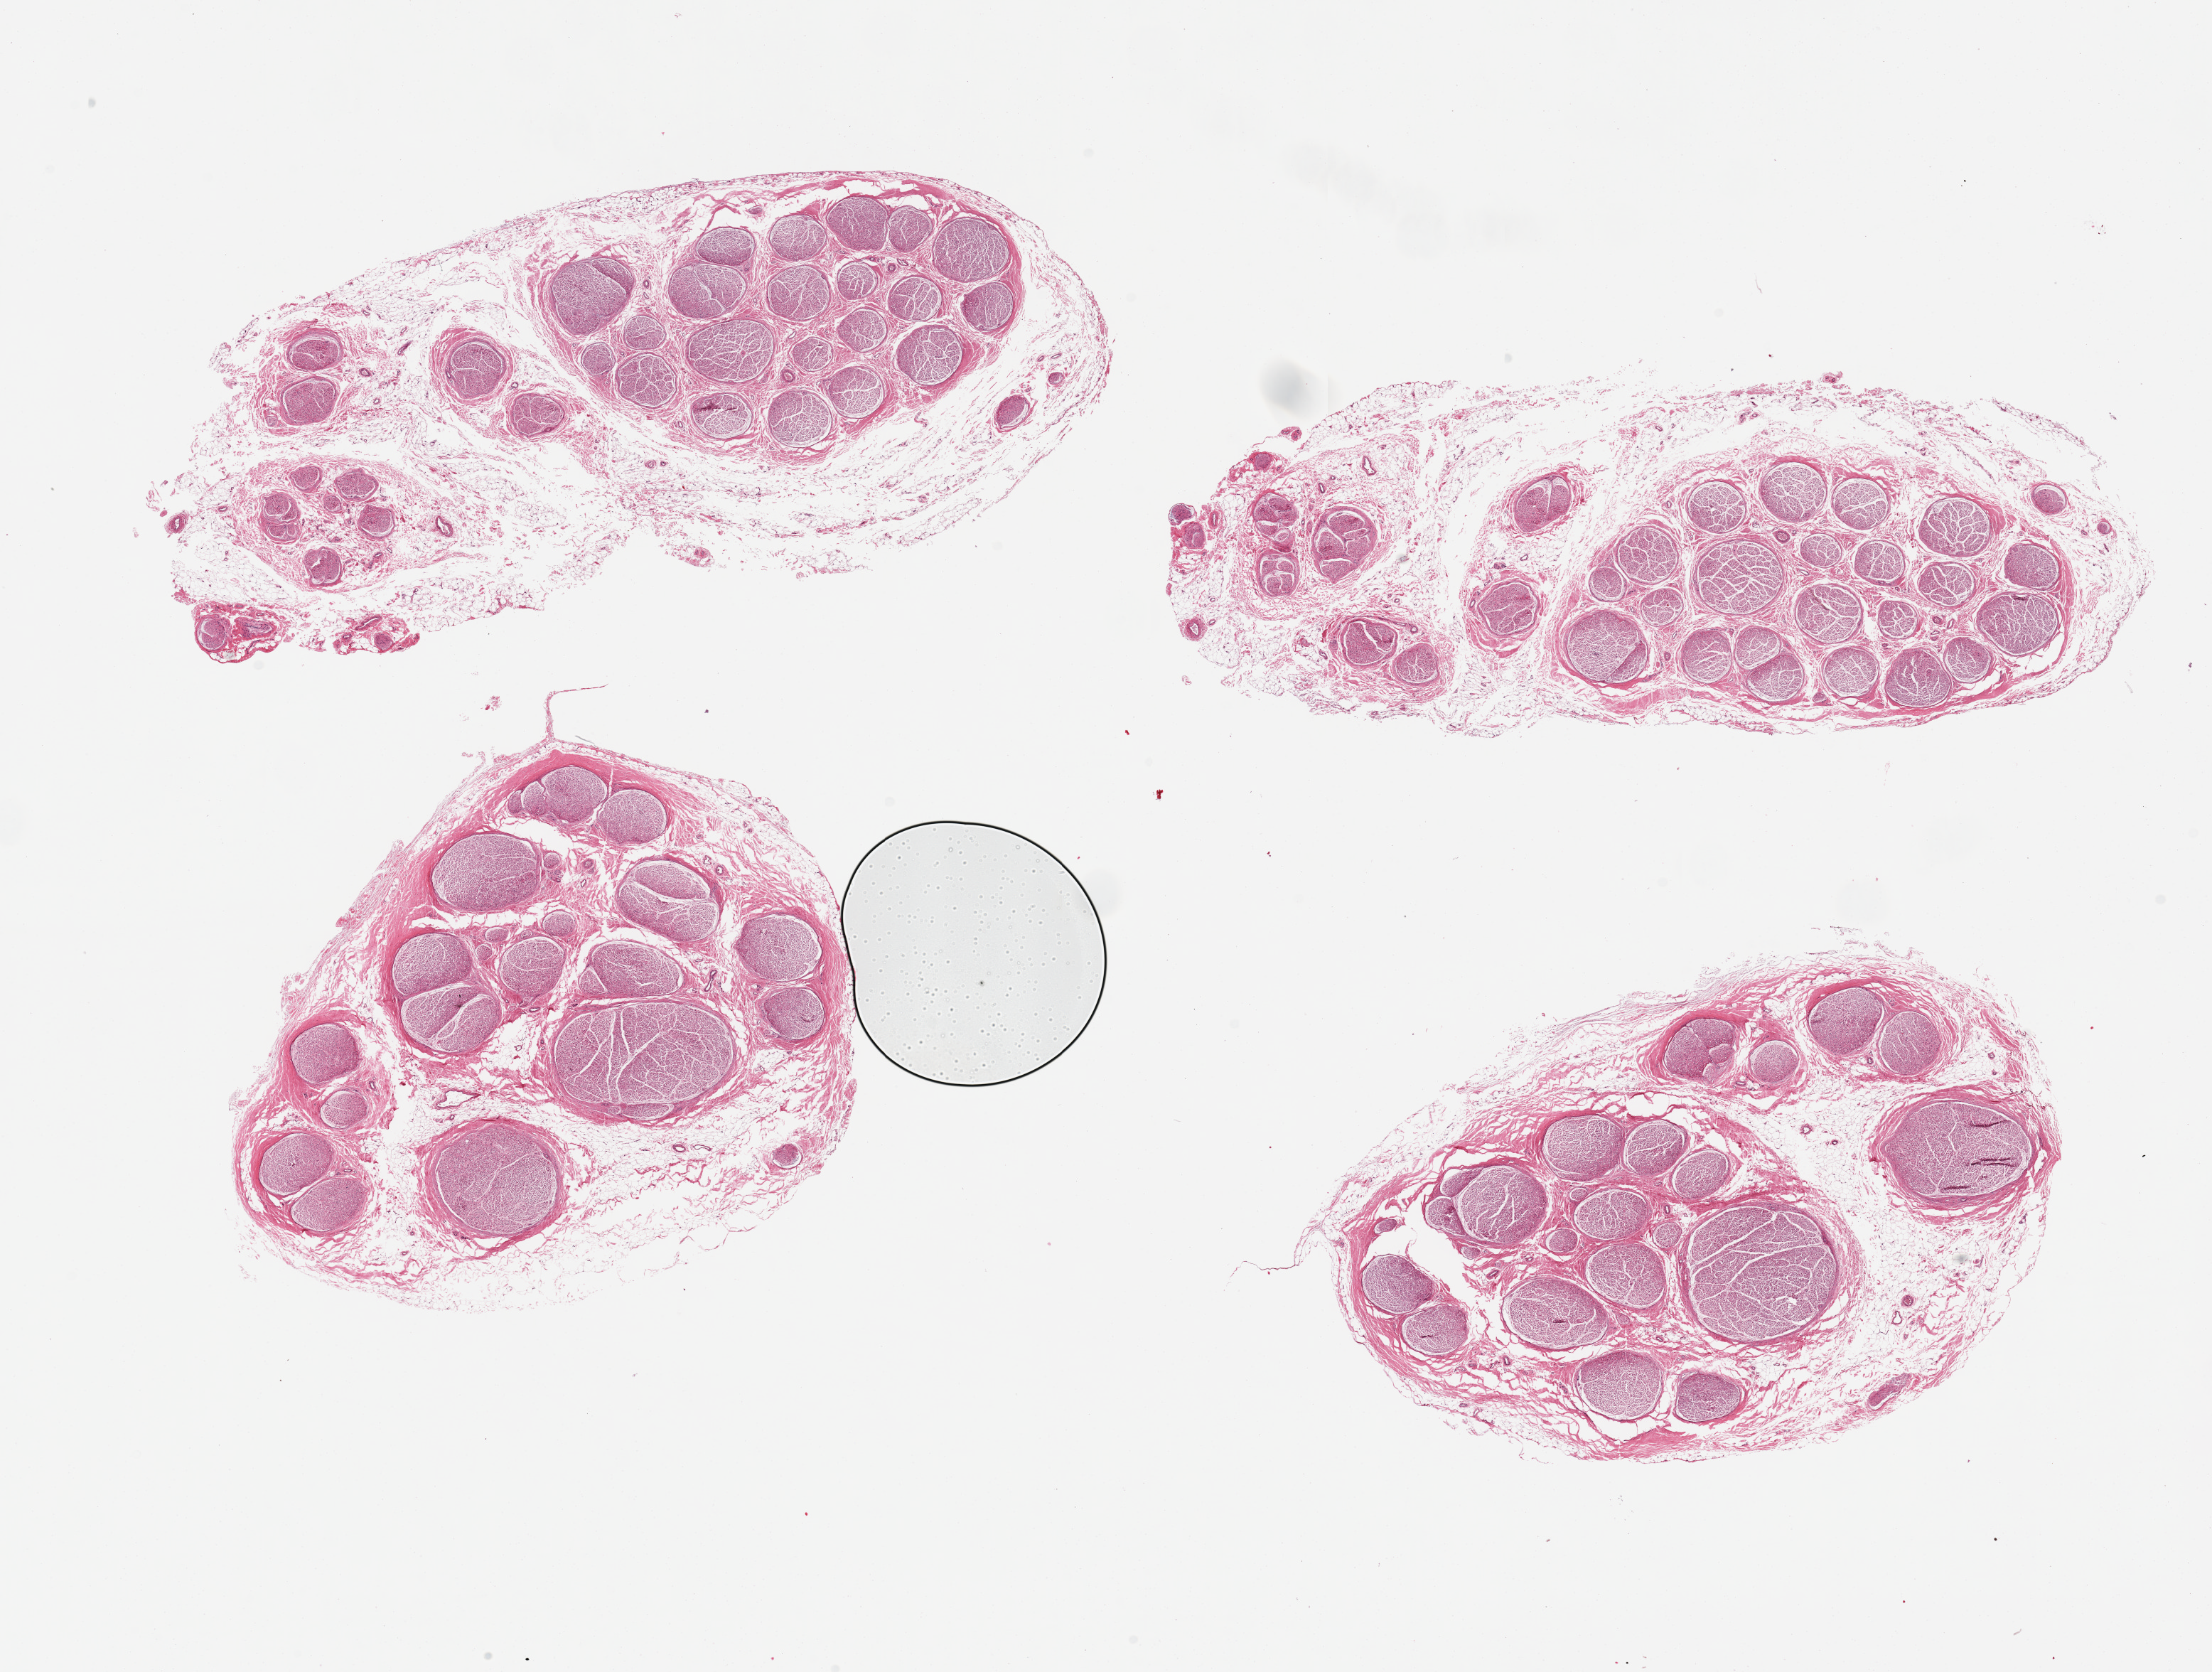
Digitized haematoxylin and eosin-stained section, brightfield — whole scanned area (about 24.6 x 18.6 mm, slide scanned at 20x) shown as a low-resolution overview, PAXgene-fixed paraffin-embedded (PFPE) section, section of tibial nerve (target tissue), donor tissue sample. Female donor.
Review note (as recorded): 4 pieces. up to 40% perineural fibroadipose tissue.